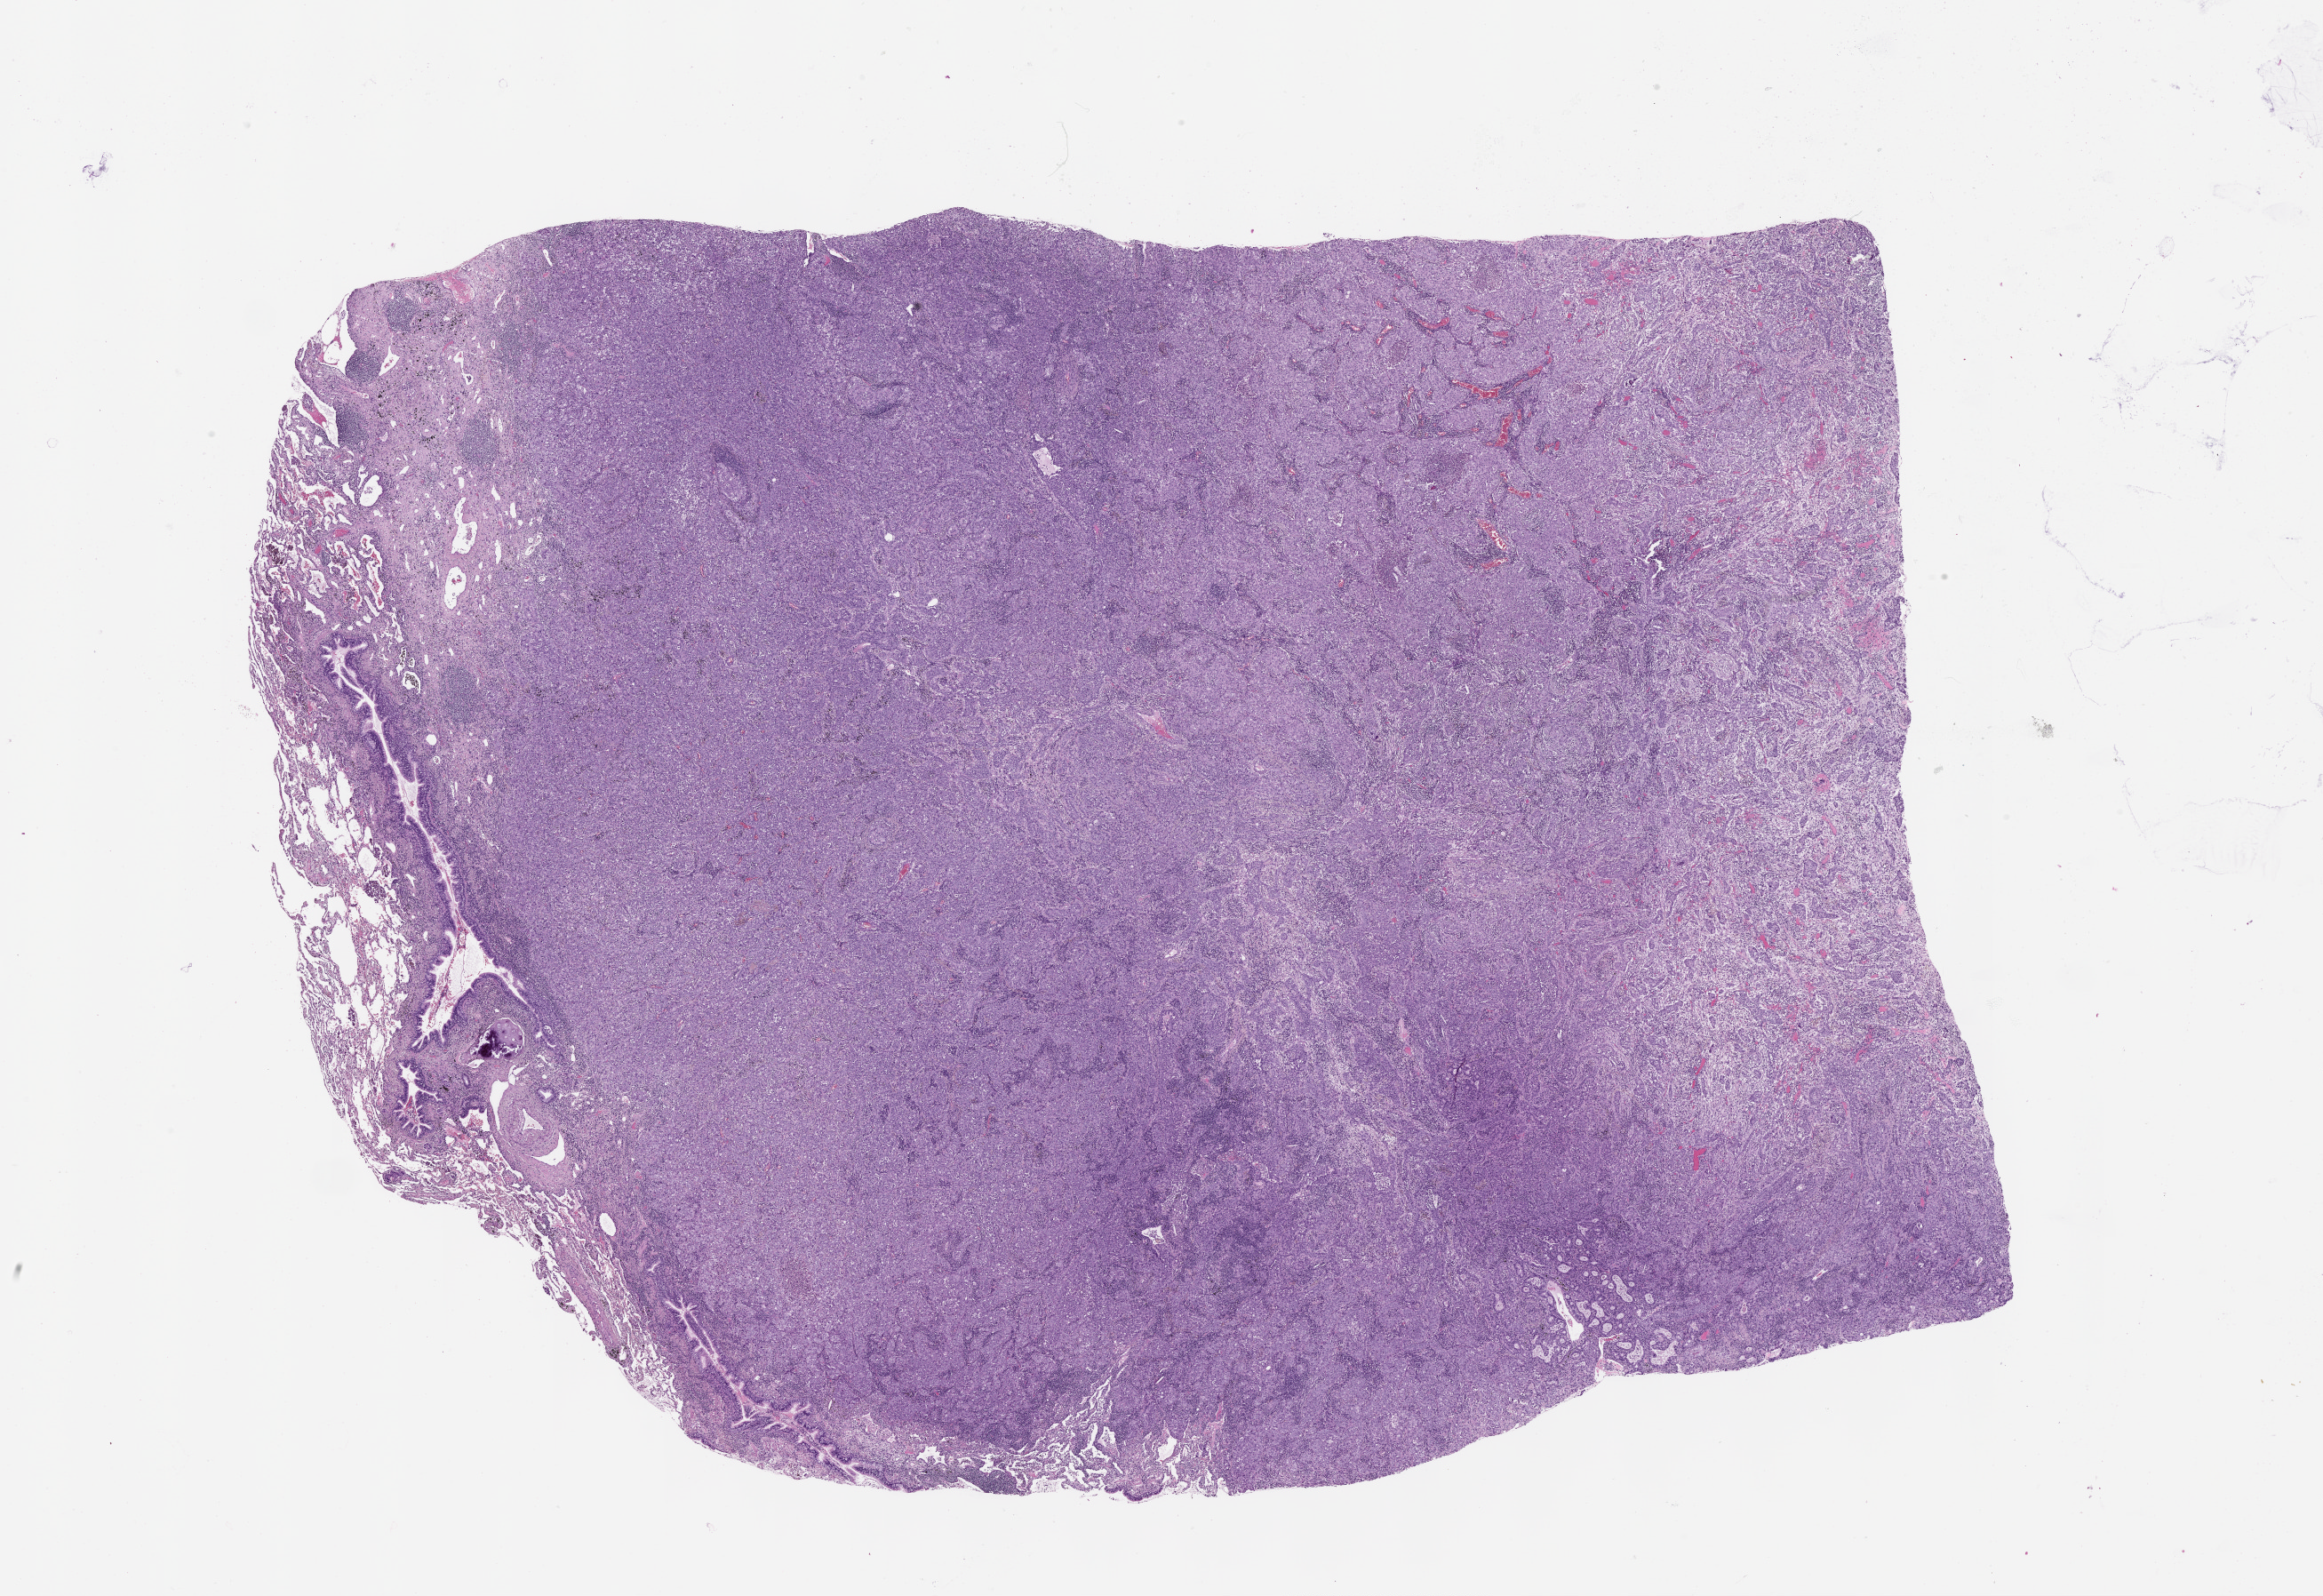
Whole-slide histology image, H&E, shown as a low-resolution overview of the whole scanned area (about 21.0 x 14.5 mm). Lung, tissue type not recorded.
• patient diagnosis (cohort enrolment): squamous cell carcinoma (lung)